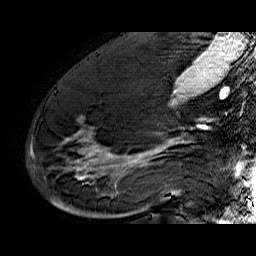
Breast MRI (dynamic contrast-enhanced), one sagittal slice; dynamic contrast-enhanced series, time point 2 of 6 at this slice position (early post-contrast); 1.5 T; TE 6.4 ms, TR 32.9 ms; 4 mm slice thickness; 256 × 256 image matrix, field of view 200 × 200 mm. Female patient. From the clinical record (not read from this slice): setting: breast cancer imaged before/during neoadjuvant chemotherapy; receptor status: HR-positive, HER2-negative.
Annotated regions visible in this slice (semi-automatic segmentation, software-assisted and operator-edited):
- analysis volume of interest (the breast-tissue region the enhancement analysis was run in; not a lesion): bounding box [x1, y1, x2, y2] px = [49, 74, 176, 210]
- tumour enhancement mask (voxels above the 100 % enhancement threshold inside the analysis volume of interest): [66, 138, 173, 179]